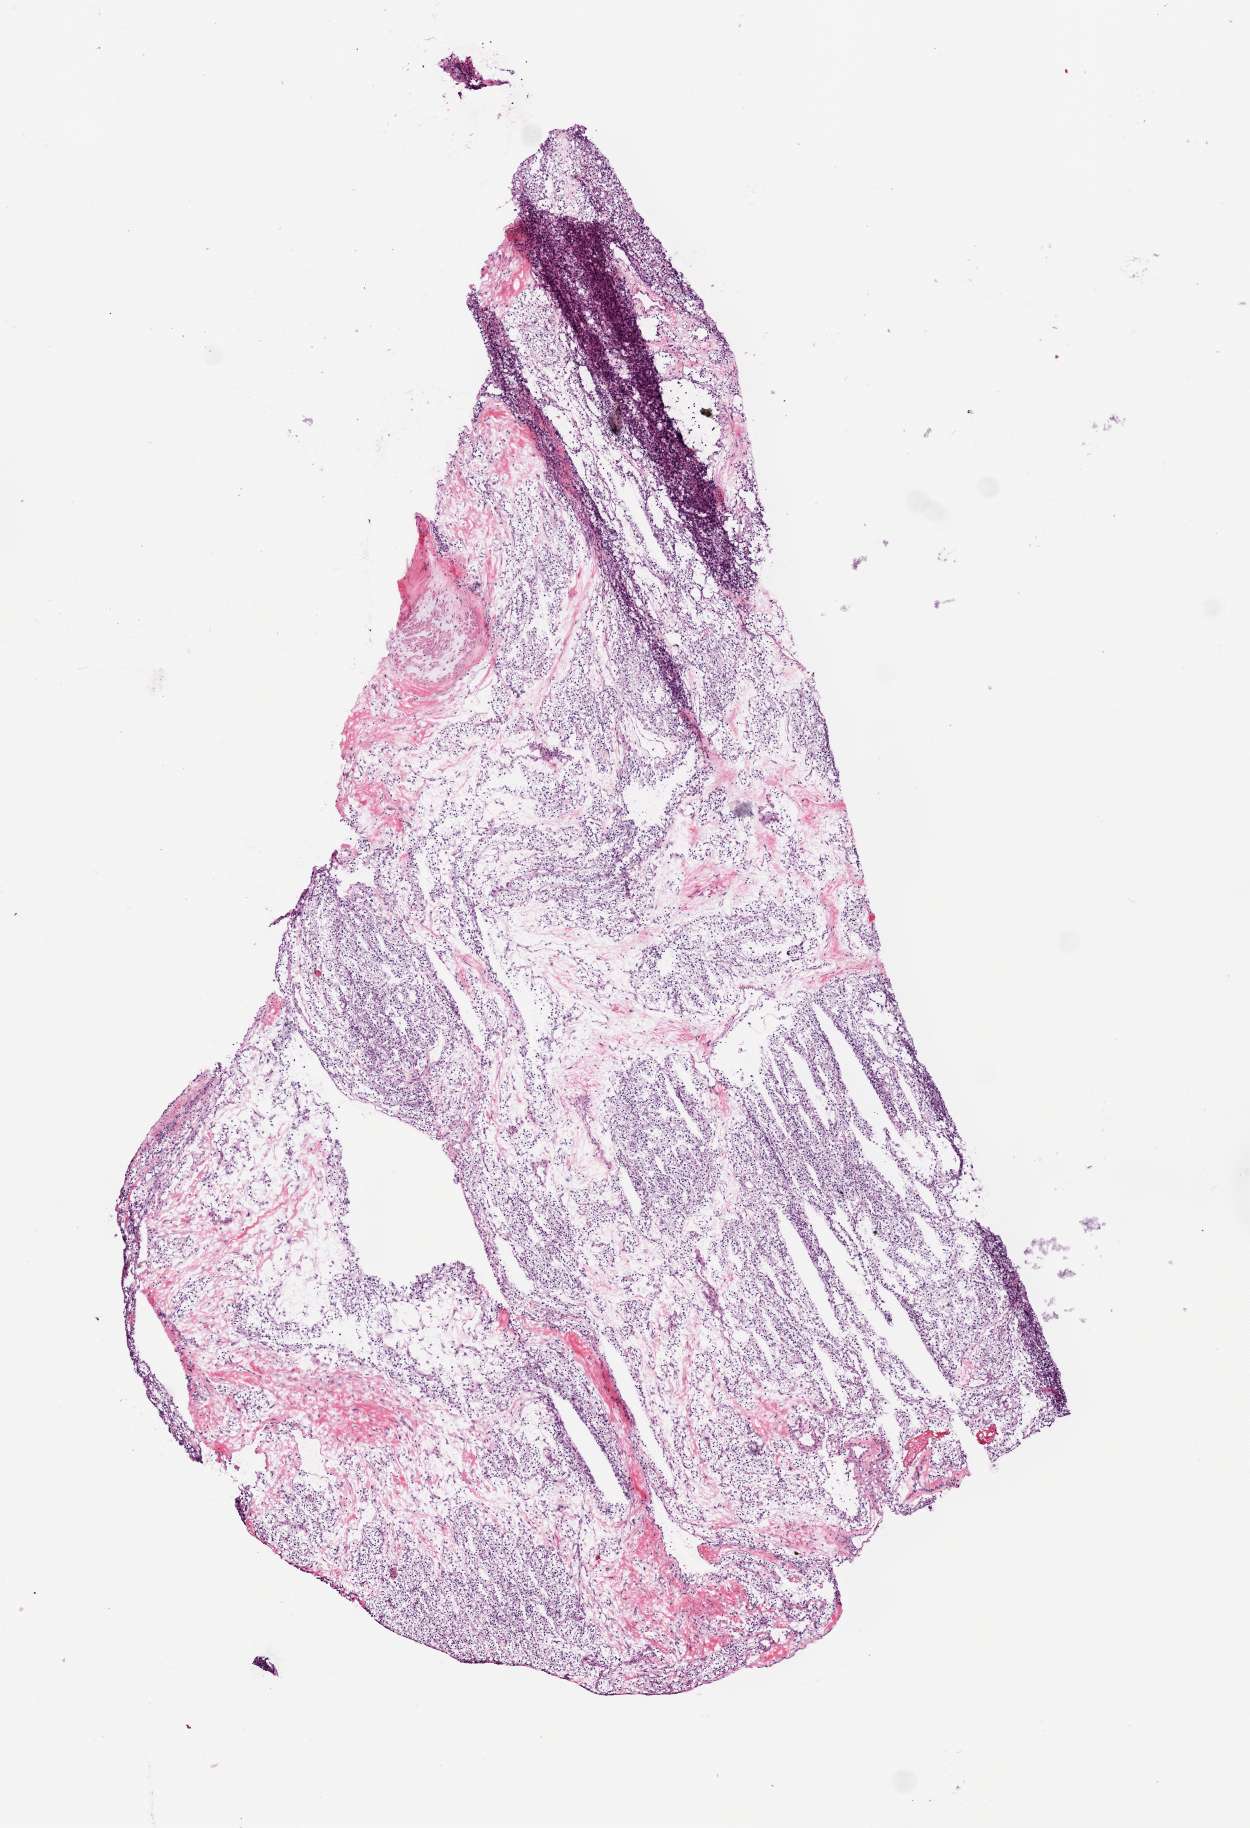
Whole-slide histology image, H&E — shown as a low-resolution overview of the whole scanned area (about 5.0 x 7.3 mm). Frozen section from the bottom of the tissue portion. Sample: primary tumour, kidney. Male, age 35 years at initial diagnosis. Histologic grade: G1 (well differentiated). Composition of this section per pathologist review: tumour cells 85%, tumour nuclei 80%, normal cells 0%, stromal cells 15%, necrosis 0%.
Pathologic diagnosis: Clear cell adenocarcinoma, NOS. AJCC pathologic stage: I (7th edition).